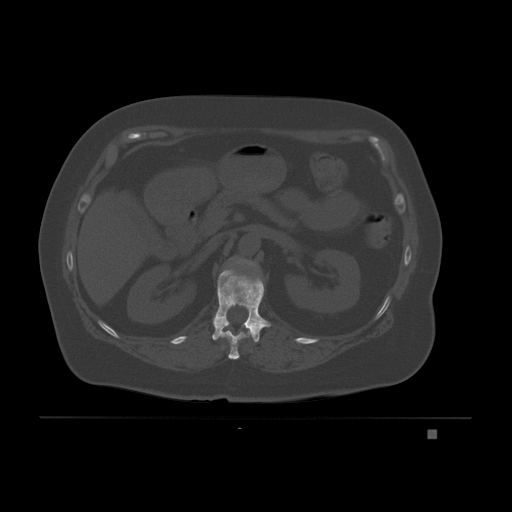
CT including the spine, one axial slice; position 81 of 221 along the scan axis; bone window (W 1800 / L 400 HU); 3 mm slice thickness; 512 × 512 image matrix, field of view 474 × 474 mm. Patient: female, 63 years. From the clinical record (not read from this slice): primary cancer: breast.
Annotated regions visible in this slice (semi-automatically segmented with operator editing):
- L1 vertebra: bounding box (x1, y1, x2, y2) in pixels: (229, 258, 256, 266)
- T11 vertebra: (215, 330, 249, 360)
- T12 vertebra: (212, 262, 271, 343)